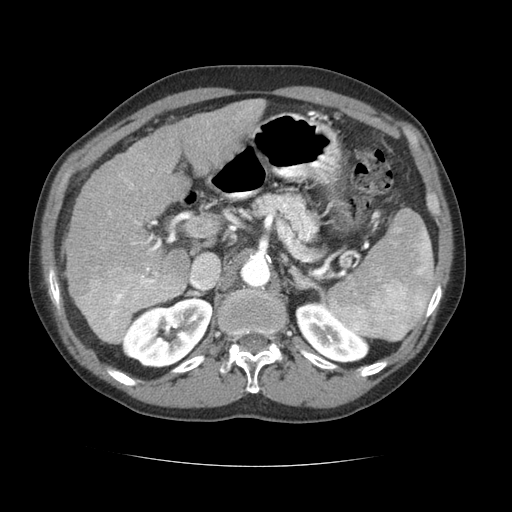
Contrast-enhanced abdominal CT (liver protocol), one axial slice. Position 42 of 69 along the scan axis. 120 kVp. Soft-tissue window (W 400 / L 40 HU). 2.5 mm slice thickness. 512 × 512 image matrix. From the clinical record (not read from this slice): diagnosis: hepatocellular carcinoma (patient treated with transarterial chemoembolisation; whether this scan precedes or follows treatment is not stated here); TNM stage (as recorded): Stage-II.
Outlined on this slice (semi-automatic segmentation, software-assisted and operator-edited):
- liver parenchyma outside the tumour (the mass and vessels are separate outlines, so this box may not span the whole liver): box from (x=64, y=98) to (x=266, y=319) px
- mass: (x=76, y=267)–(x=185, y=344)
- liver vessels: (x=109, y=180)–(x=159, y=272)